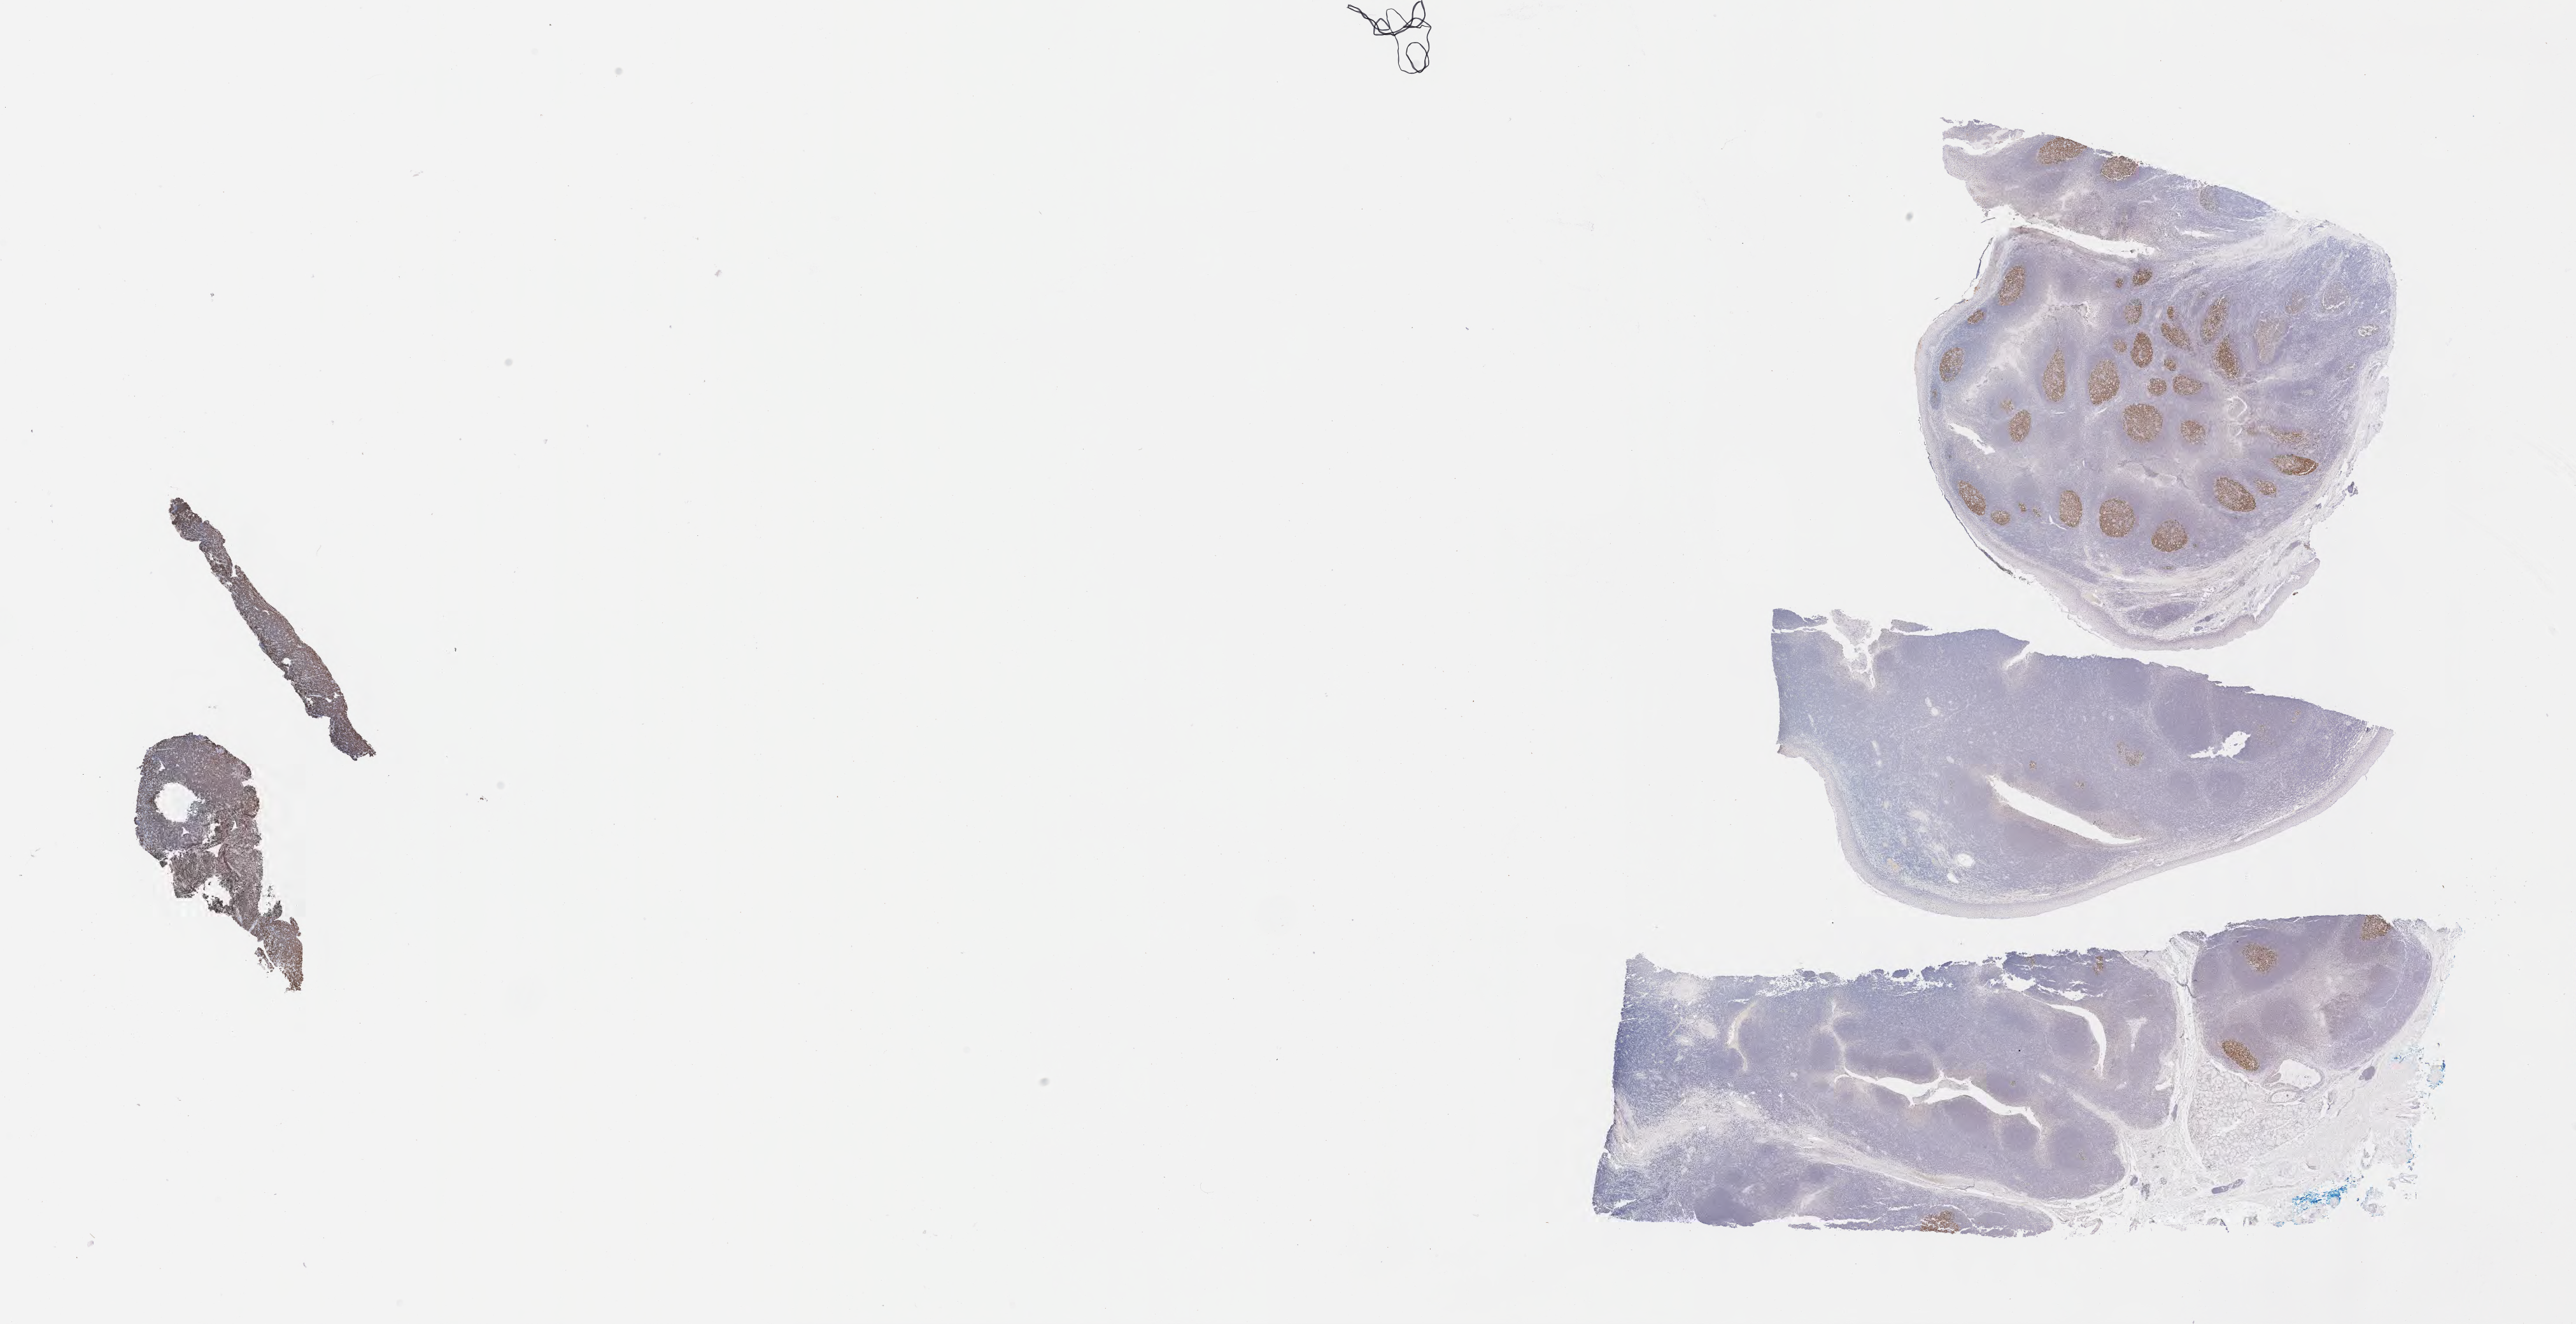
IHC for BCL6, whole-slide image — low-resolution overview of the scanned area, about 32.7 x 16.8 mm, specimen: tumor tissue. Patient: male, age at initial diagnosis 8 years.
- diagnosis: Burkitt lymphoma, NOS